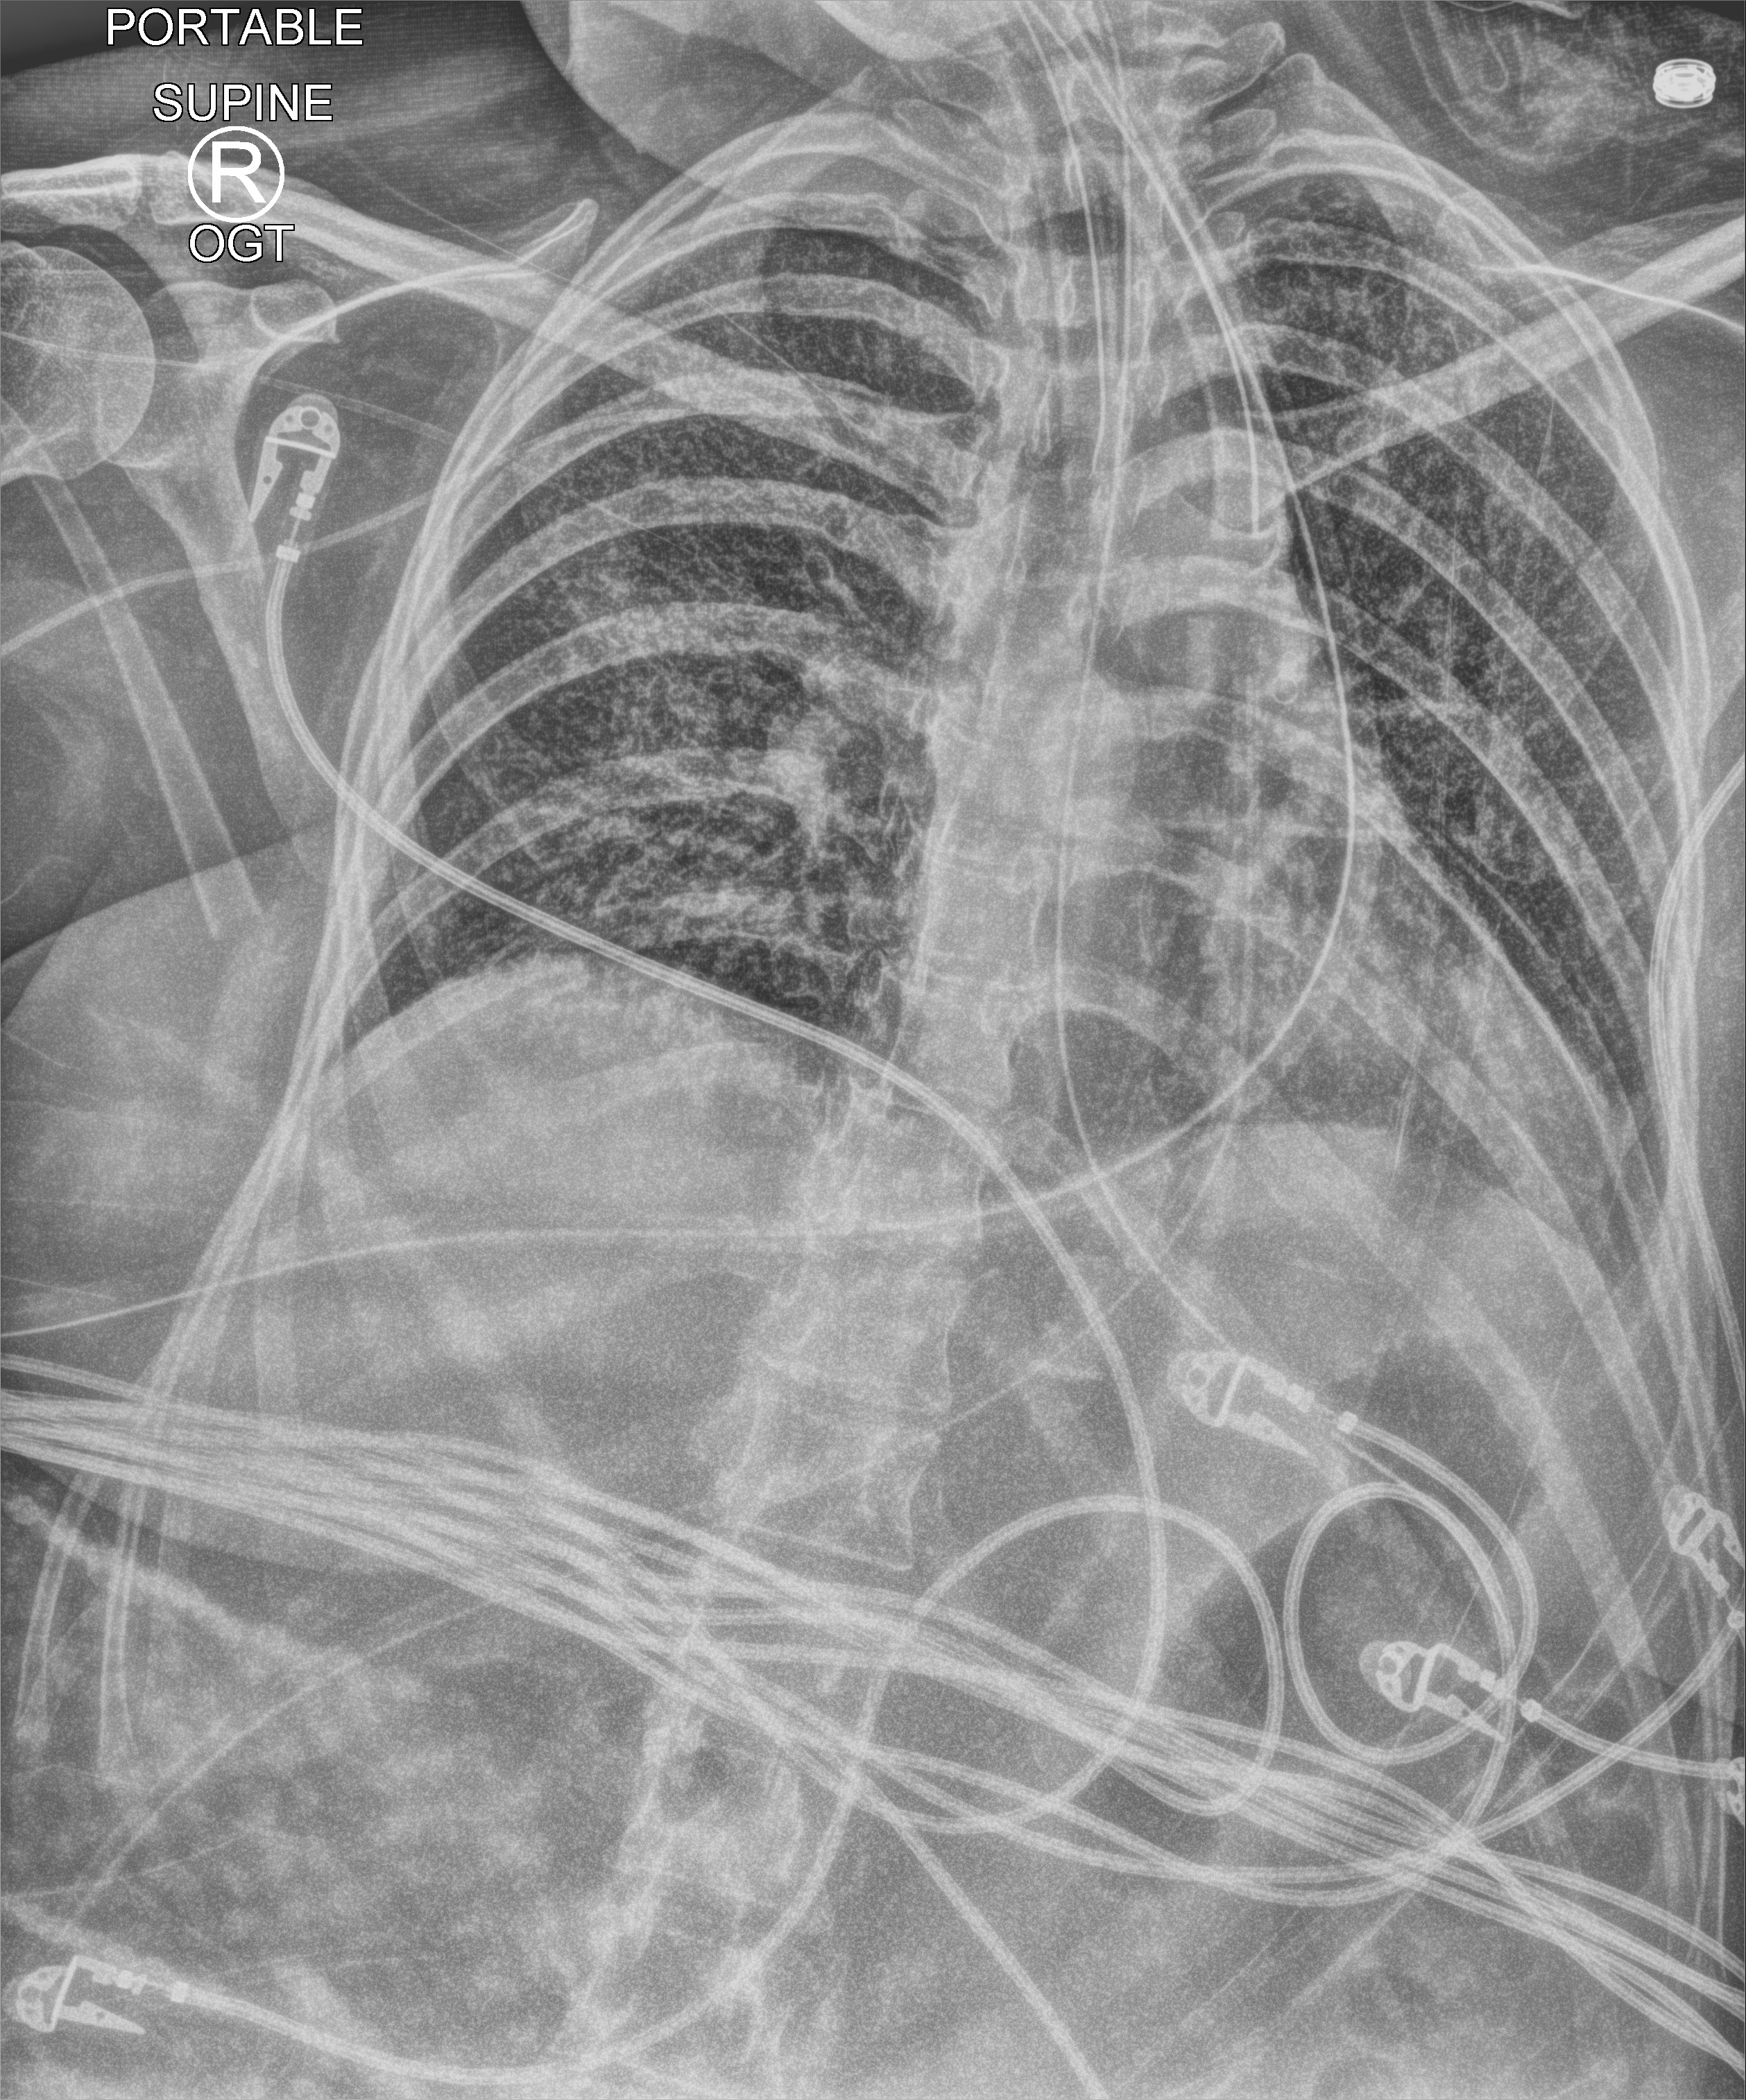
Bedside chest radiograph (computed radiography); anteroposterior (AP) projection. Female patient hospitalised with COVID-19, age 18–59 years.
Admission-level facts for this patient (not findings on this image; timing relative to this image not recorded):
- COPD (admission record): no